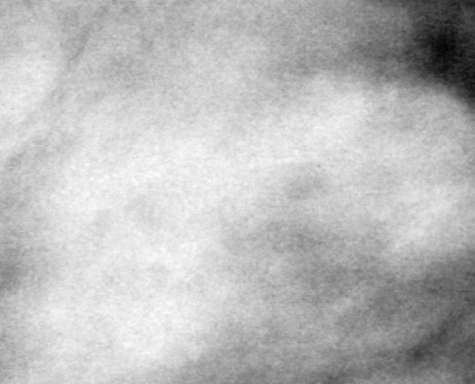
Cropped region of a digitized screen-film mammogram centred on a radiologist-marked abnormality; left breast; CC view; BI-RADS breast density category 3 (scale 1–4).
- Marked abnormality: mass, shape lobulated, margins obscured; BI-RADS assessment category 4; subtlety rating 2 on a 1 (subtle) to 5 (obvious) scale; pathology (as recorded): benign.